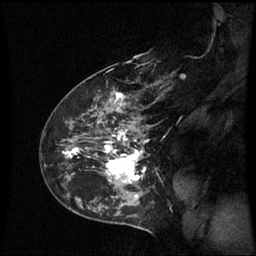
Breast MRI (dynamic contrast-enhanced), one sagittal slice; position 41 of 60 along the scan axis; dynamic contrast-enhanced series, image 2 of 3 at this slice position (ordered by acquisition); 1.5 T; TE 4.2 ms, TR 8.9 ms; 2.3 mm slice thickness; 256 × 256 image matrix, field of view 210 × 210 mm. Female patient, age 43 years. From the clinical record (not read from this slice): setting: breast cancer imaged before/during neoadjuvant chemotherapy; receptor status: HER2-positive.
Outlined on this slice (semi-automatic segmentation, software-assisted and operator-edited):
- analysis volume of interest (the breast-tissue region the enhancement analysis was run in; not a lesion): bounding box (x1, y1, x2, y2) in pixels: (56, 80, 160, 195)
- tumour enhancement mask (voxels above the 70 % enhancement threshold inside the analysis volume of interest): (63, 94, 149, 185)